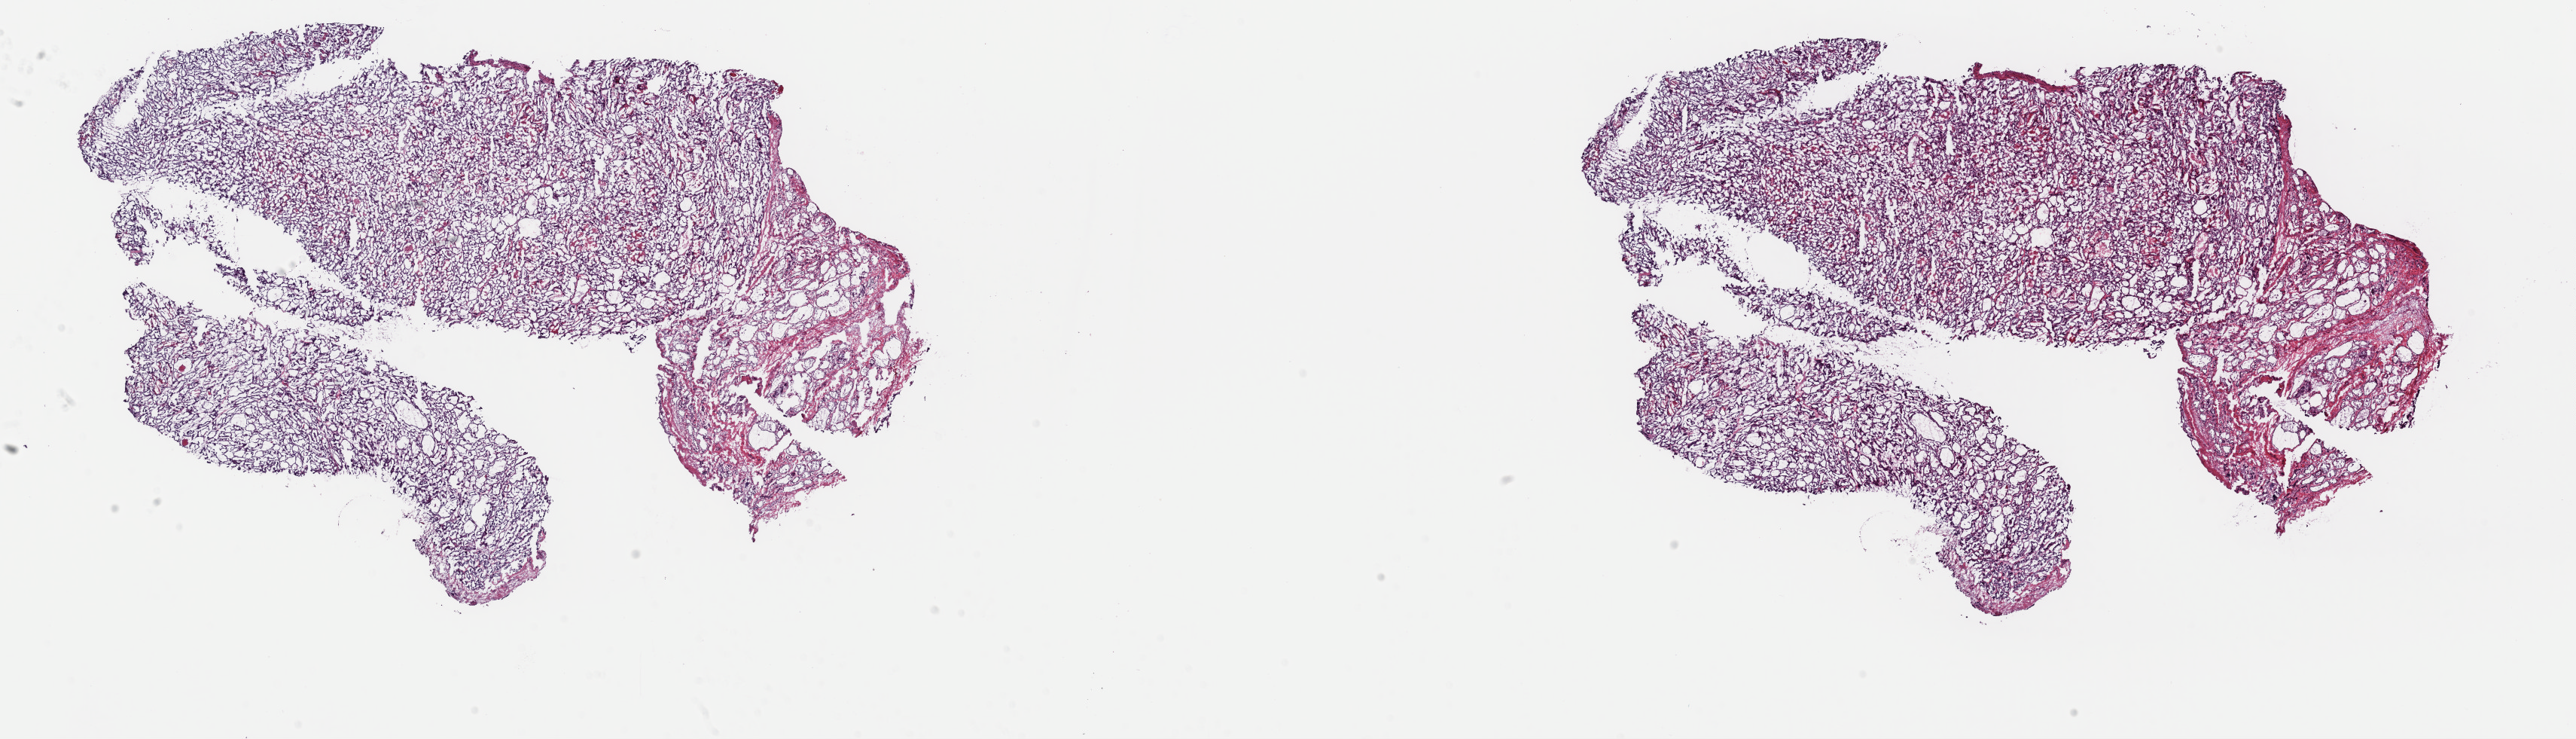
Digitized H&E tissue section (whole slide), low-resolution overview of the scanned area, about 27.0 x 7.7 mm (slide scanned at 40x). Frozen section from the top of the tissue portion. Primary tumour sample from the thyroid. Female patient; age at initial diagnosis 55 years. Composition of this section per pathologist review: tumour cells 85%, tumour nuclei 100%, normal cells 0%, stromal cells 15%, necrosis 0%. Infiltration values recorded for this section: lymphocyte infiltration 0%, monocyte infiltration 1%, neutrophil infiltration 0%.
AJCC pathologic stage: II (6th edition). Pathologic diagnosis: Papillary adenocarcinoma, NOS (thyroid gland).